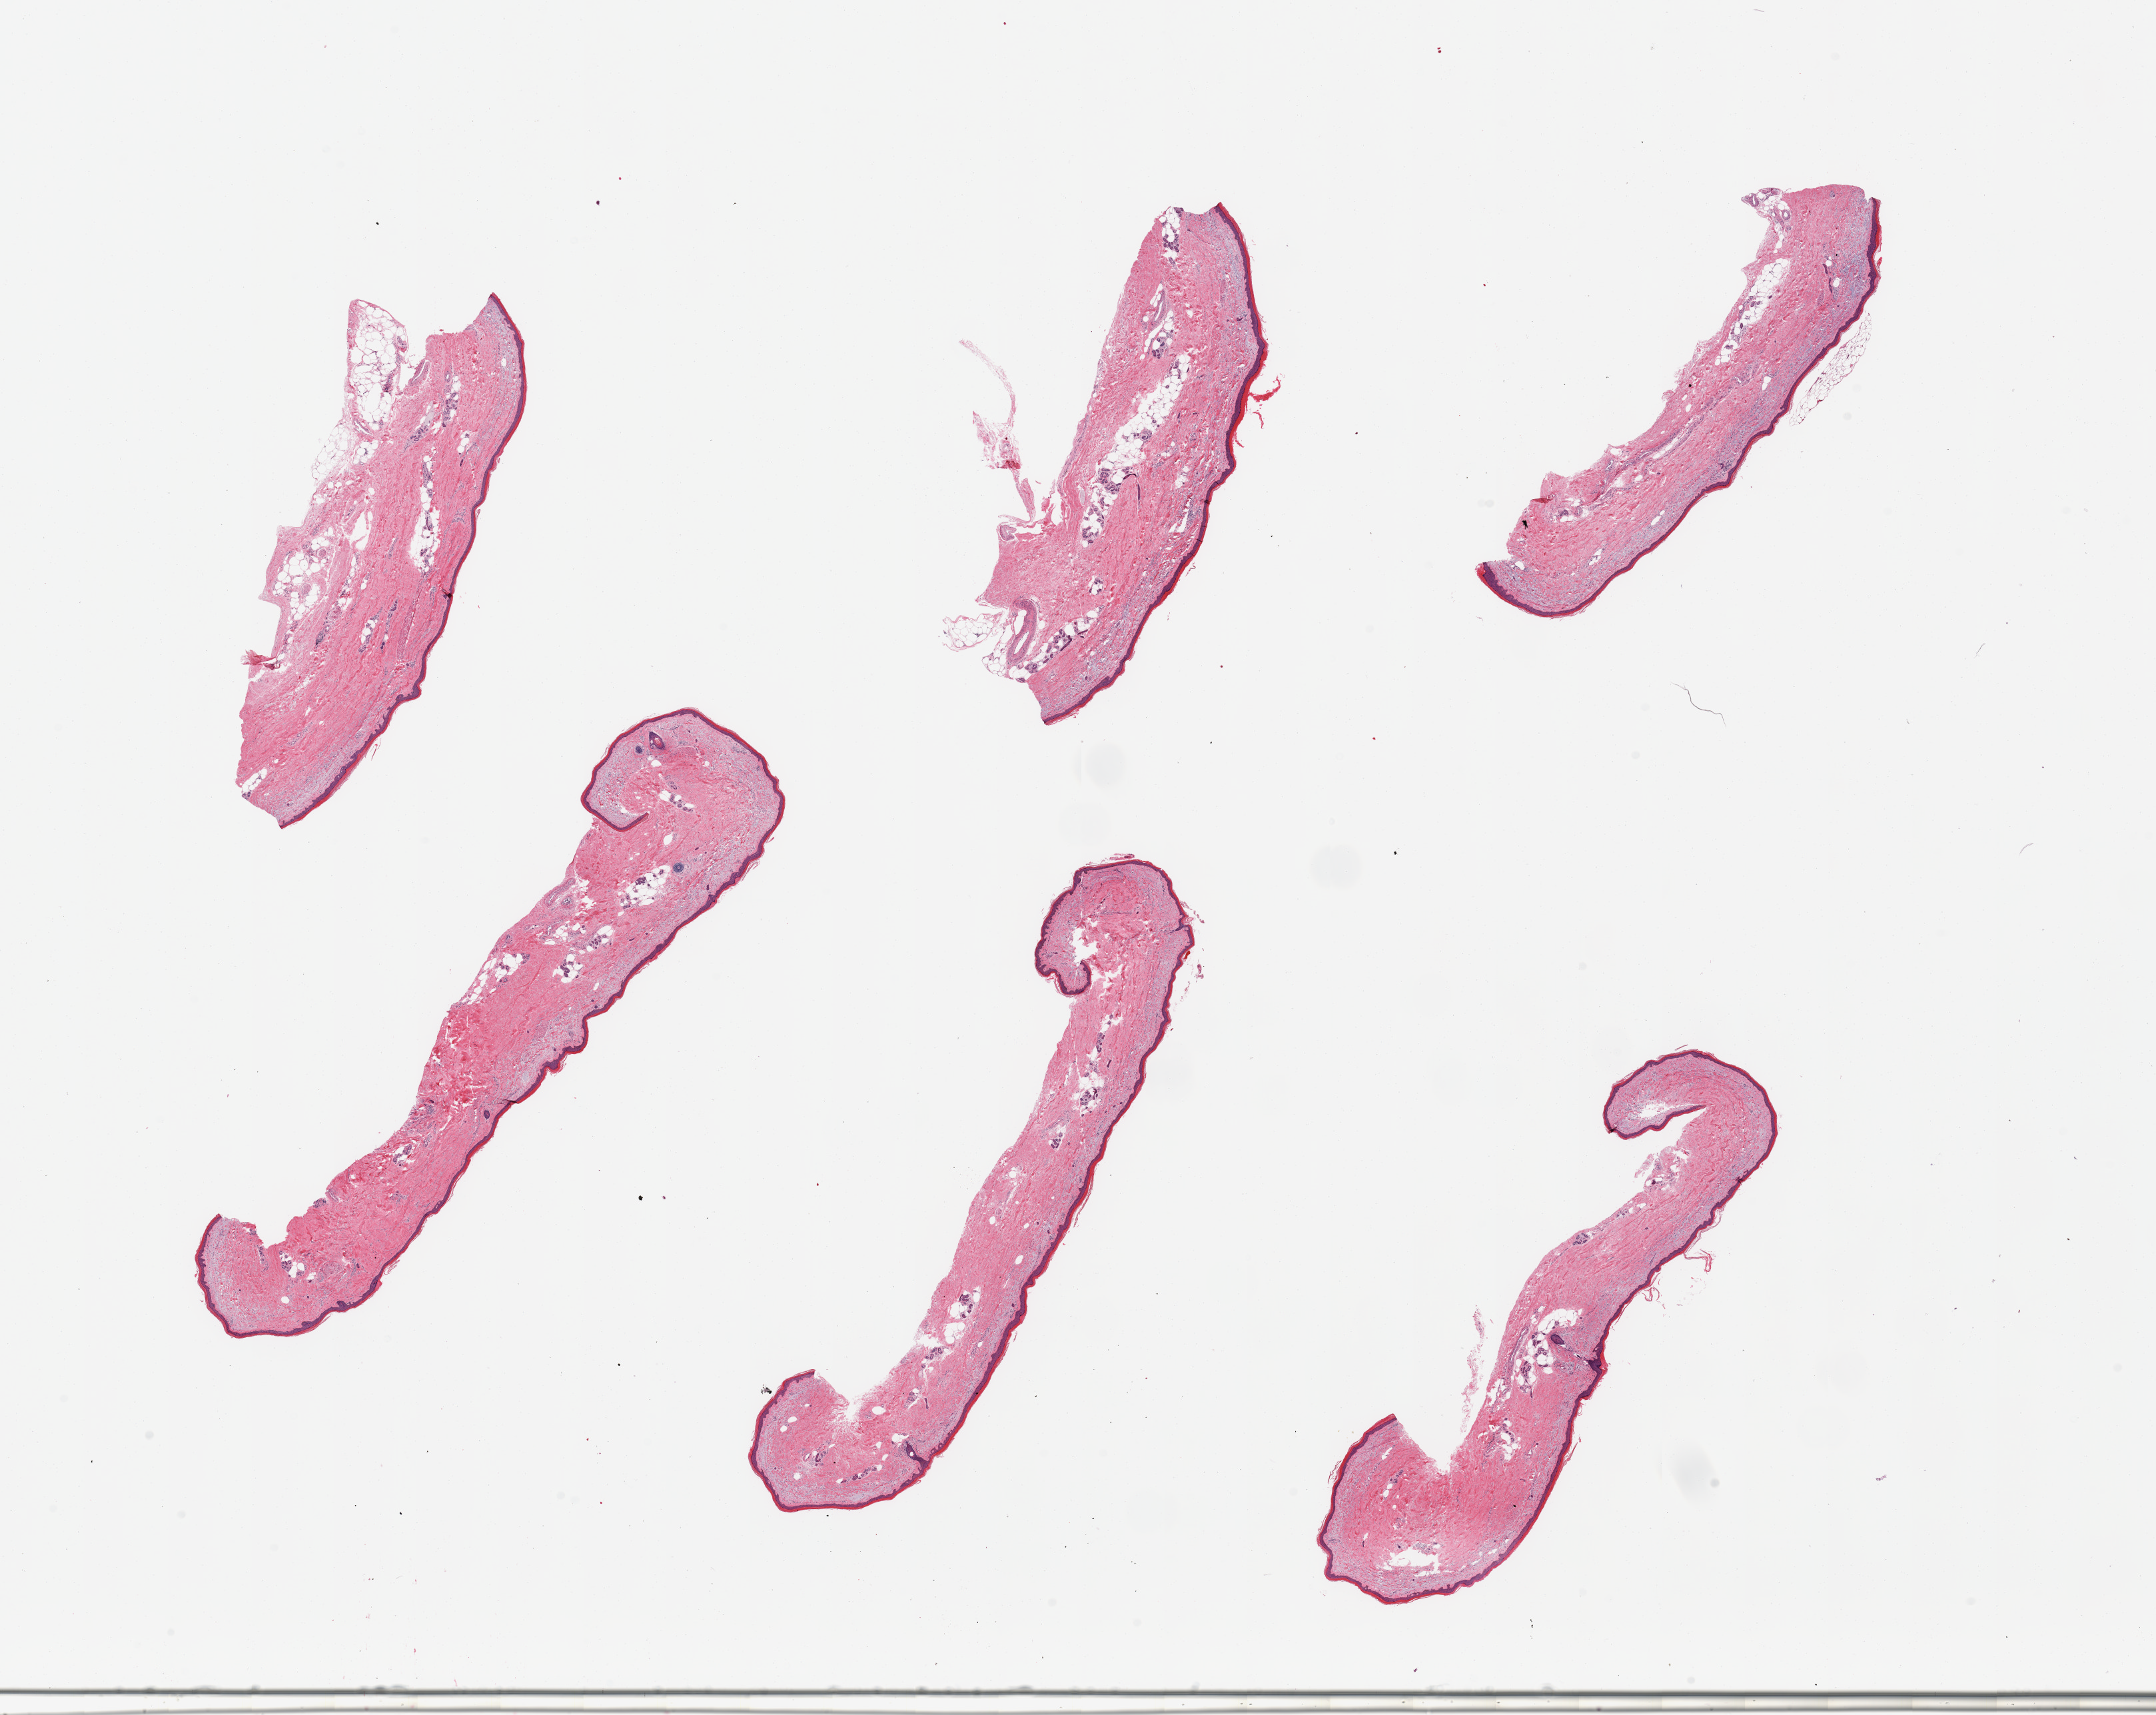
Digitized haematoxylin and eosin-stained section — whole scanned area (about 25.6 x 20.4 mm, acquisition: 20x scan) shown as a low-resolution overview. PAXgene-fixed paraffin-embedded (PFPE) section. Sampled site (target tissue): skin of lower leg. Donor tissue sample. Donor sex: female.
Review note (as recorded): 6 pieces, trace dermal fat; prominent solar elastosis in dermis; squamous epithelium is ~30-40 microns.